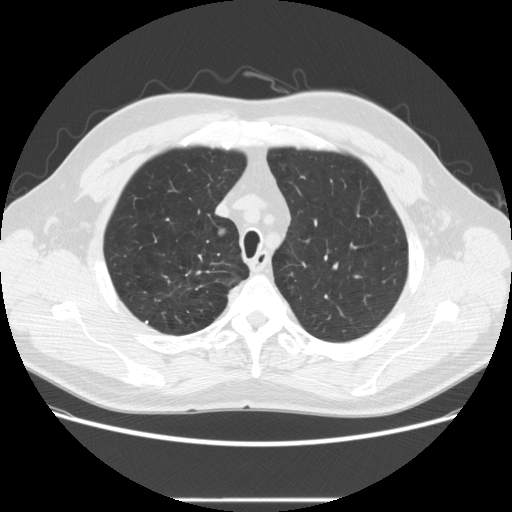
Low-dose screening chest CT, axial slice. First (baseline) screen. Lung window (W 1500 / L -600 HU). 2.5 mm slice thickness. Slice 50 of 270 in the series. 512 × 512 image matrix. Male participant, aged 64 years at enrolment. Former smoker at enrolment.
- Expert-annotated lung lesion, bounding box [x1, y1, x2, y2] px = [191, 220, 240, 256].
- The screening reader recorded 2 non-calcified nodules or masses ≥4 mm on this exam; which of them this box marks is not recorded.
- Official screen result: positive, change unspecified: nodule(s) >= 4 mm or enlarging nodule(s), mass(es), or other non-specific abnormalities suspicious for lung cancer.
- Participant outcome: lung cancer diagnosed 753 days after this screen — adenocarcinoma, NOS, right upper lobe, moderately differentiated (G2), stage IA (AJCC 6th edition), 14 mm at pathology.